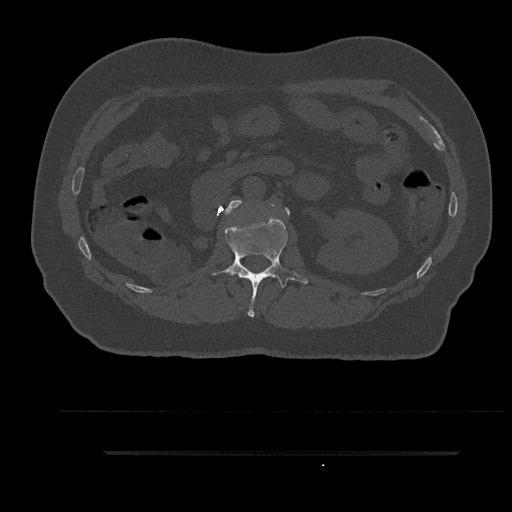
CT including the spine, one axial slice; position 166 of 797 along the scan axis; bone window (W 1800 / L 400 HU); 0.5 mm slice thickness; 512 × 512 image matrix, field of view 432 × 432 mm. Patient: male, 63 years. From the clinical record (not read from this slice): primary cancer: renal; vertebrae with lytic lesions (as recorded): T8.
Annotated regions visible in this slice (semi-automatic segmentation, software-assisted and operator-edited):
- L1 vertebra: bounding box (x1, y1, x2, y2) in pixels: (212, 216, 308, 317)
- L2 vertebra: (224, 200, 290, 216)